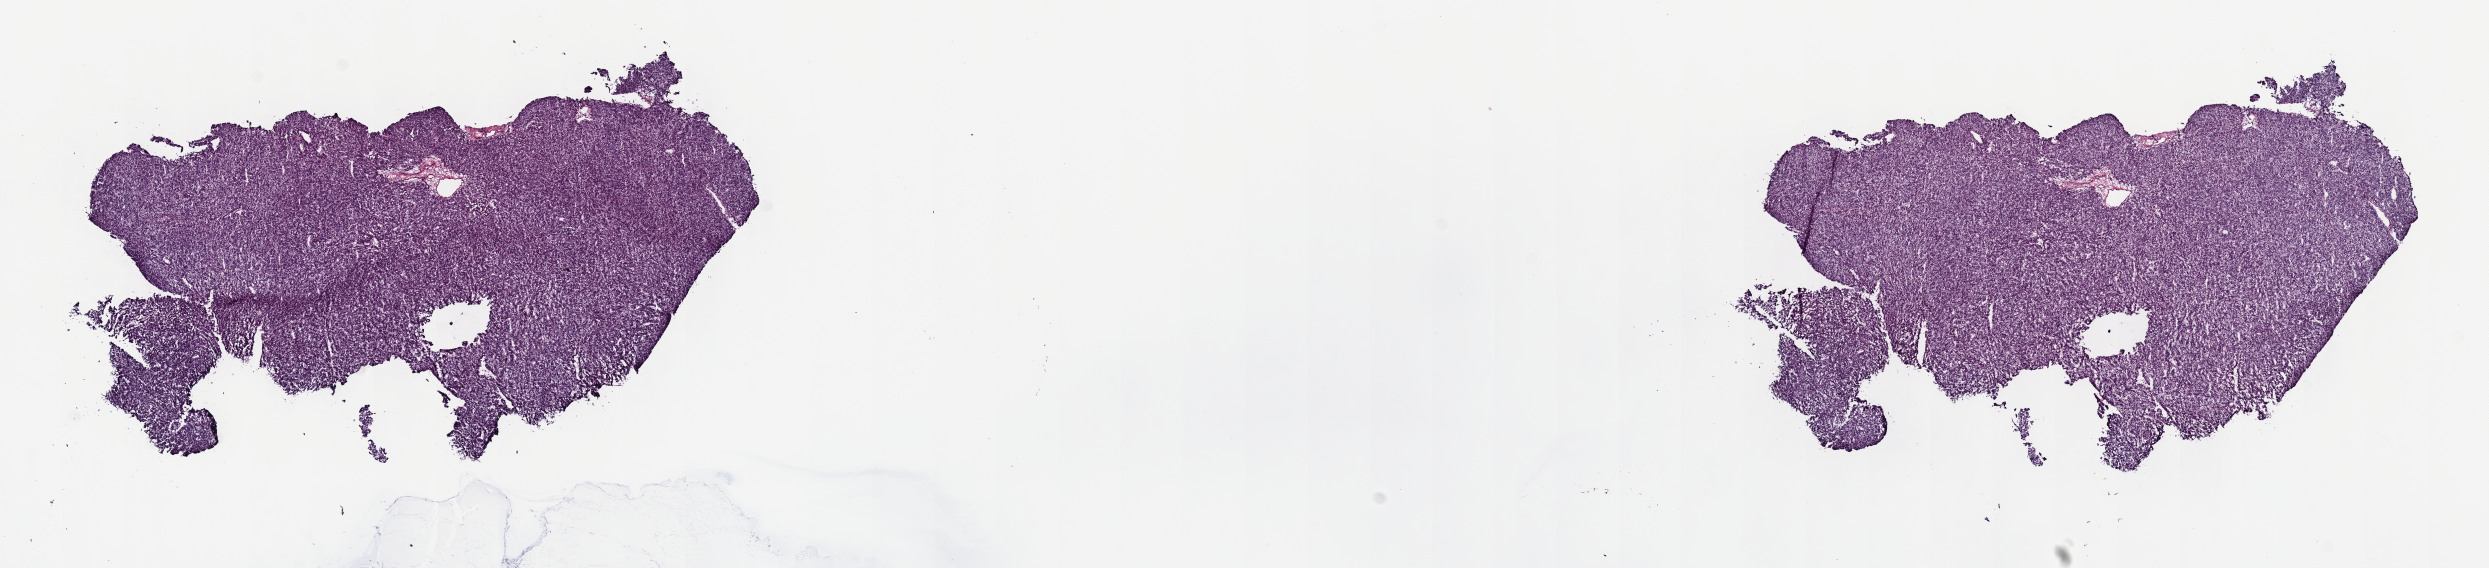
H&E whole-slide image — low-resolution overview of the scanned area, about 20.1 x 4.6 mm (acquisition: 40x scan). Frozen section from the top of the tissue portion. Primary tumour sample from the liver. Male, age 43 years at initial diagnosis. Histologic grade: G3 (poorly differentiated). Composition of this section per pathologist review: tumour cells 100%, tumour nuclei 95%, normal cells 0%, stromal cells 0%, necrosis 0%. Inflammatory infiltration, as recorded: lymphocyte infiltration 0%, monocyte infiltration 0%, neutrophil infiltration 0%.
• TNM: T1 N0 M0
• diagnosis: Hepatocellular carcinoma, NOS
• AJCC pathologic stage: I (7th edition)